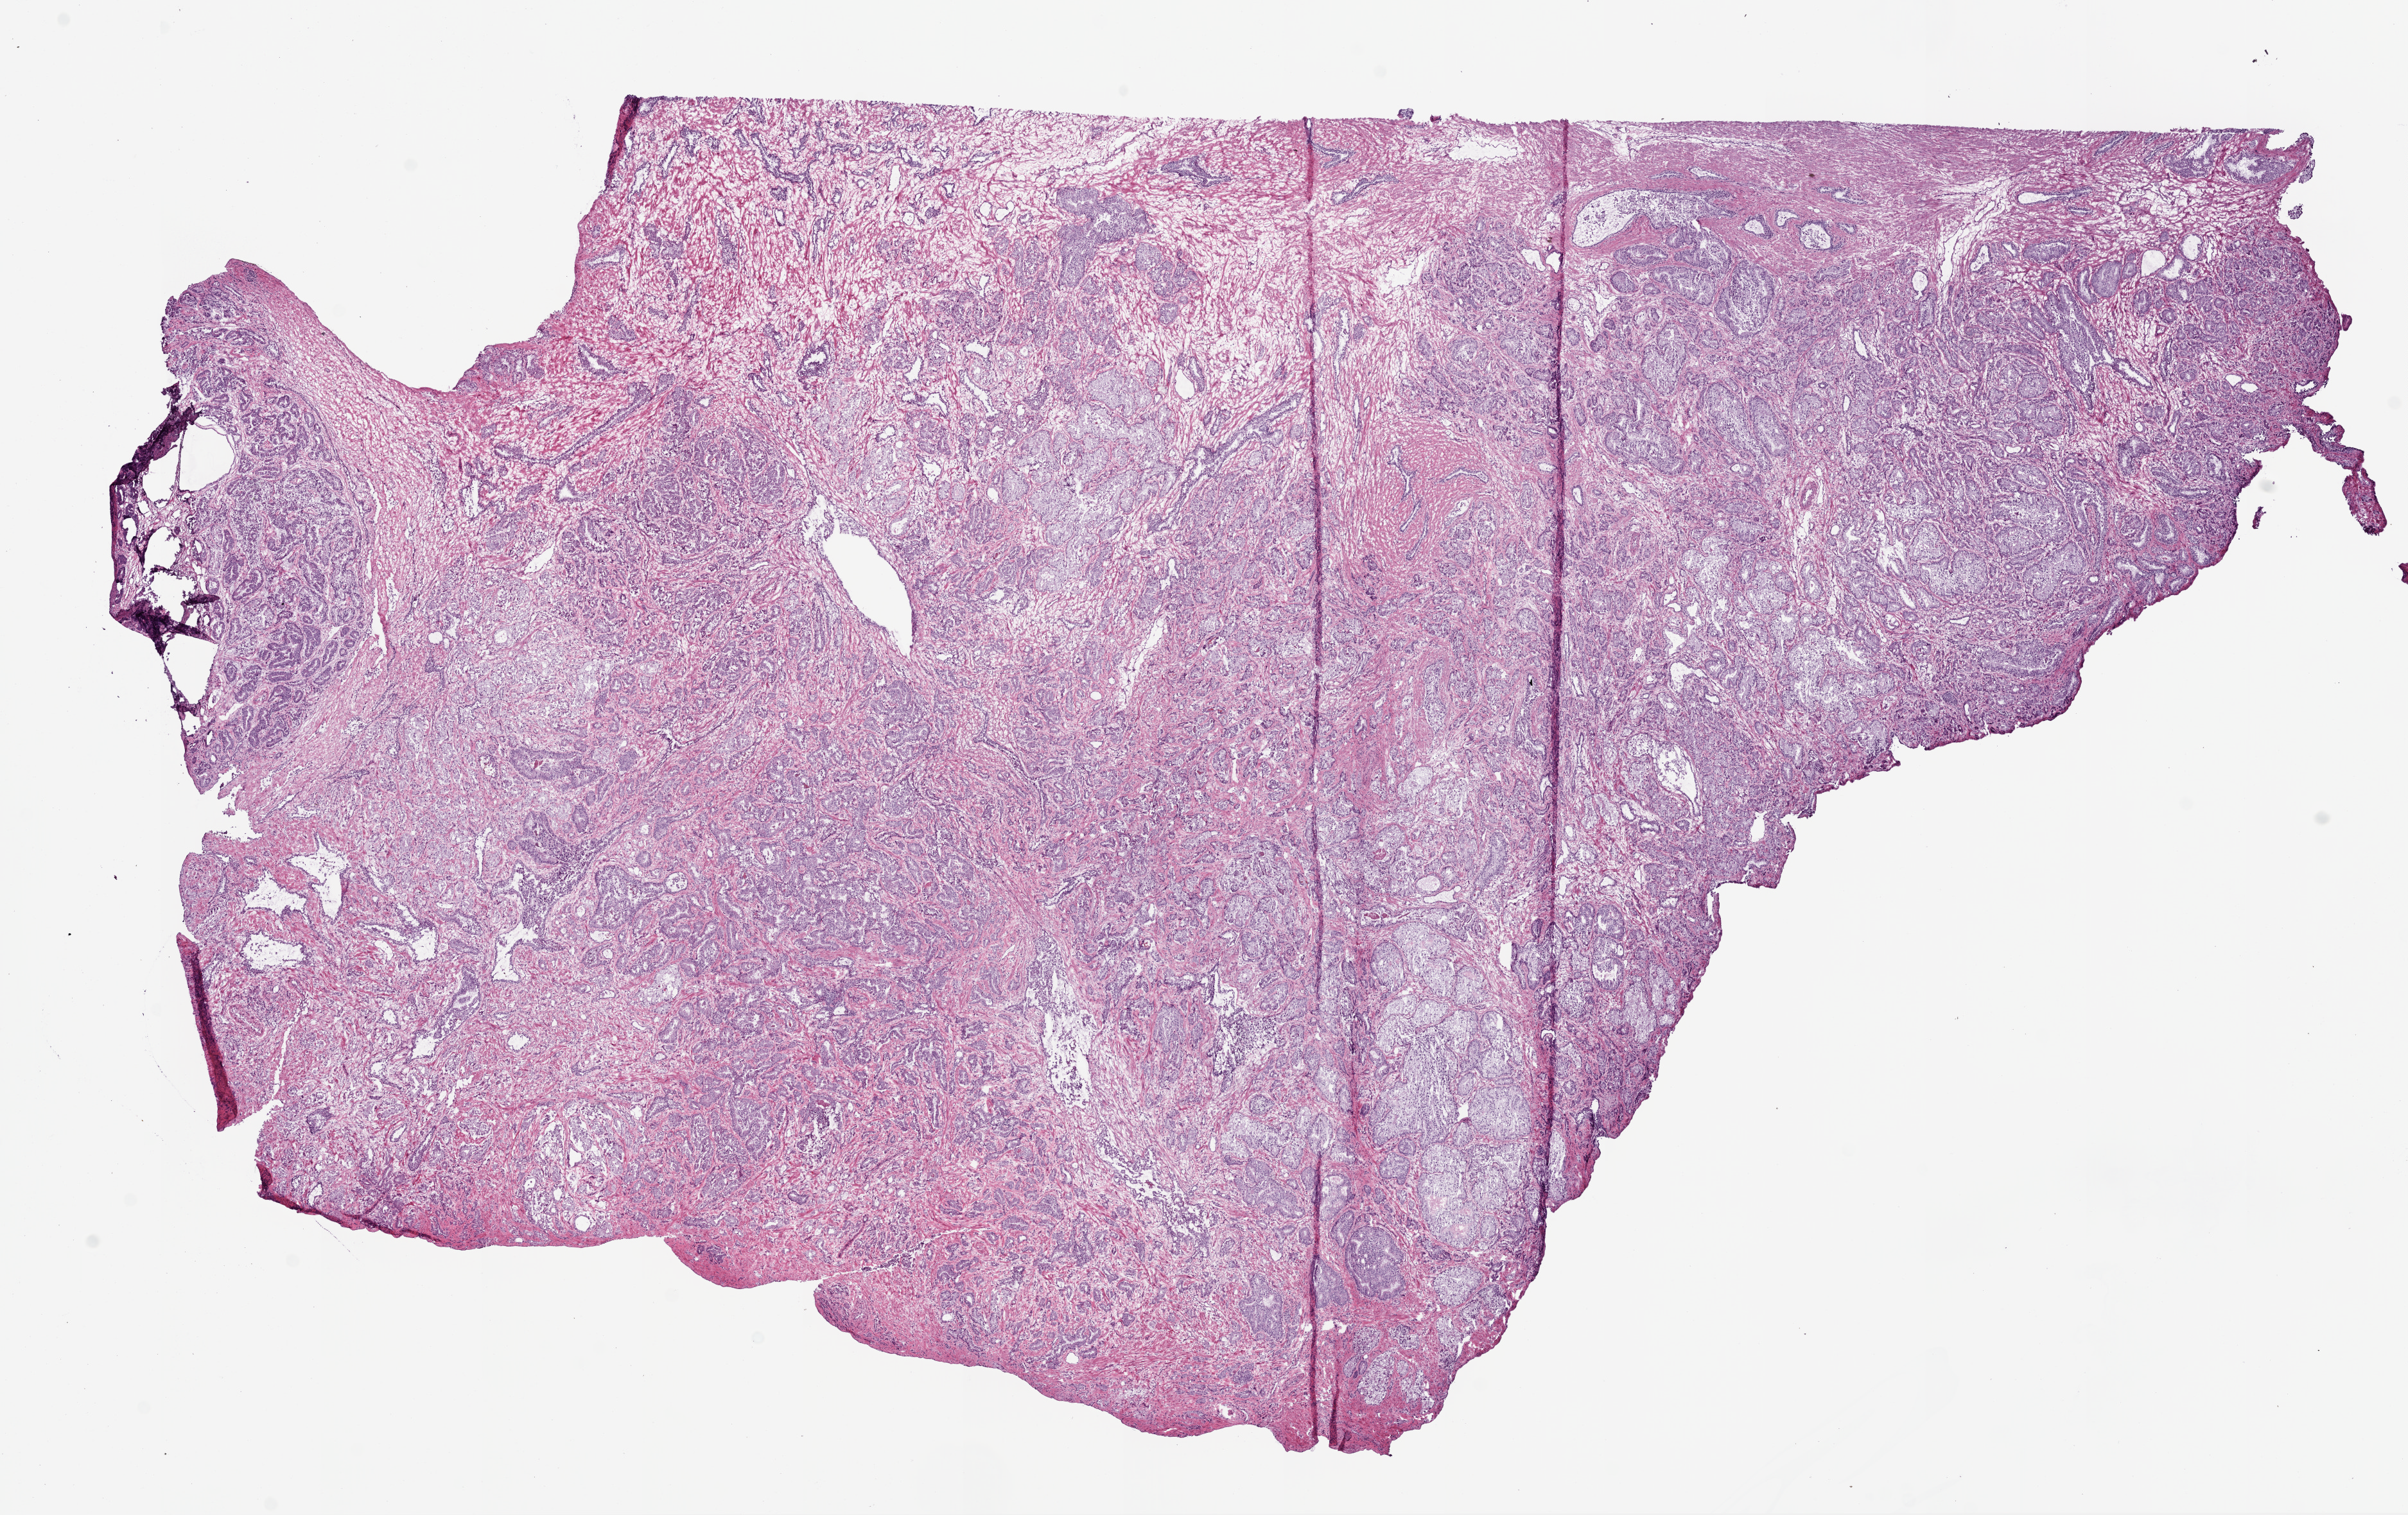
Hematoxylin and eosin (H&E) stained whole-slide image, low-resolution overview of the scanned area, about 15.0 x 9.5 mm (from a 20x scan); frozen section; primary tumour sample from the prostate. Male patient; age at initial diagnosis 49 years.
Histologic diagnosis: Acinar cell carcinoma (prostate gland).